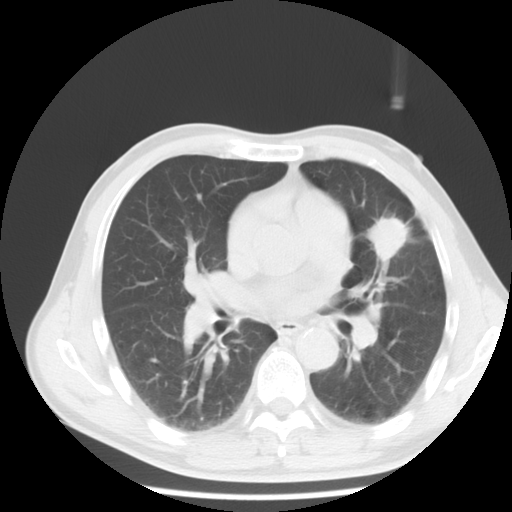
Chest CT, one axial slice; position 5 of 10 along the scan axis; reconstruction kernel STANDARD; lung window (W 1500 / L -600 HU); 5 mm slice thickness; 512 × 512 image matrix. Male patient, age 54 years. Case-level facts recorded for this patient, not image findings: clinical TNM (as recorded): T1c N0 M0.
Annotated regions visible in this slice (rectangle marked by the reading radiologist):
- lung tumour (recorded histology: adenocarcinoma): bounding box <366,204,408,269> (left, top, right, bottom; pixels)